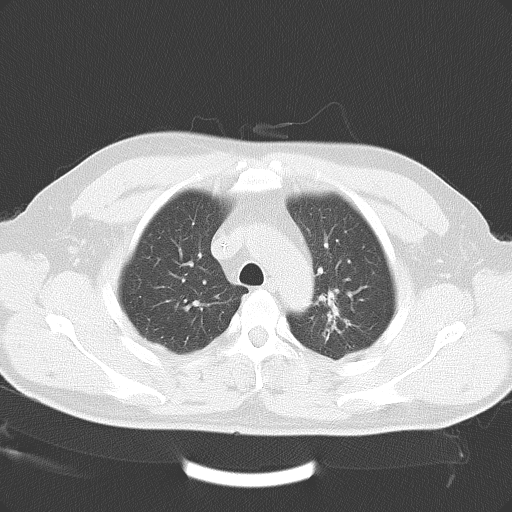
Chest CT, one axial slice; position 30 of 41 along the scan axis; reconstruction kernel B70f; 120 kVp; lung window (W 1500 / L -600 HU); 512 × 512 image matrix, field of view 362 × 362 mm. Patient: male, 45 years. Case-level facts recorded for this patient, not image findings: clinical TNM (as recorded): T2 N0 M0.
Structures marked on this image (rectangle marked by the reading radiologist):
- lung tumour (recorded histology: adenocarcinoma): bounding box <316,286,360,349> (left, top, right, bottom; pixels)